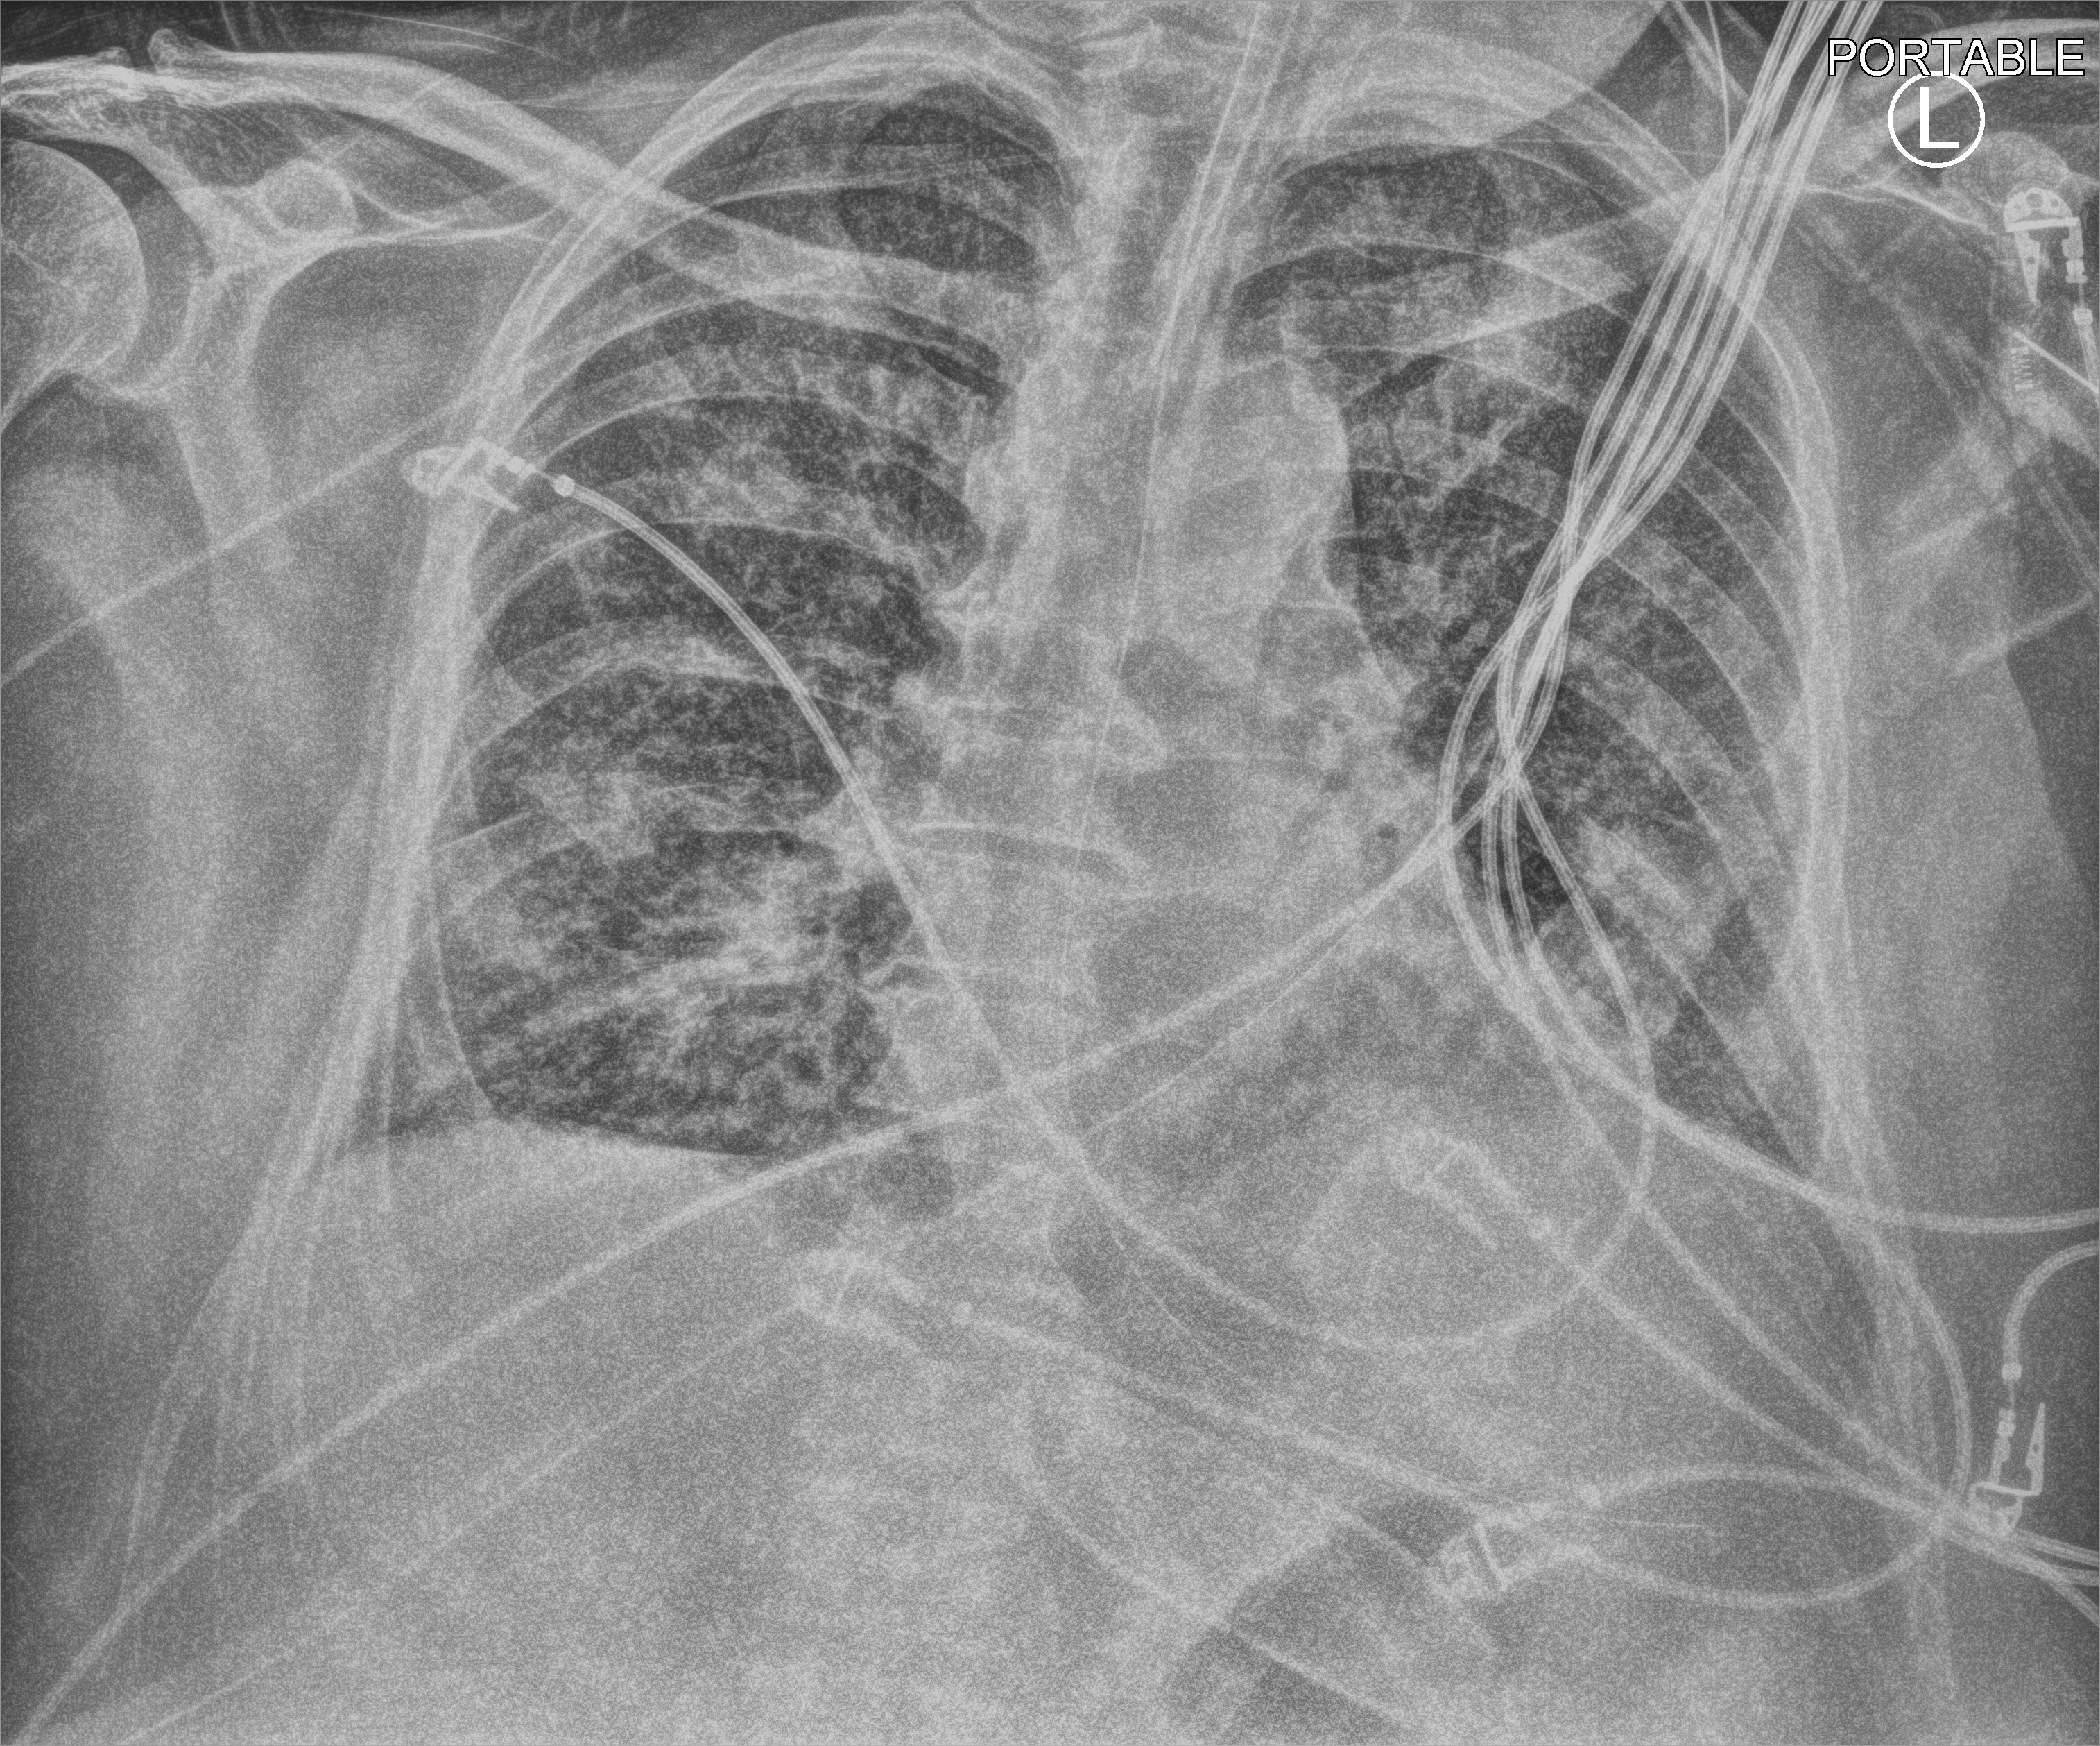
Portable chest radiograph, anteroposterior (AP) projection. Patient hospitalised with COVID-19; male, aged 60–74 years.
From the hospital-stay record, not from the radiograph (when in the stay this image was taken is not recorded):
- mechanically ventilated during this hospital stay: yes
- other chronic lung disease (admission record): no
- admitted to intensive care during this hospital stay: yes